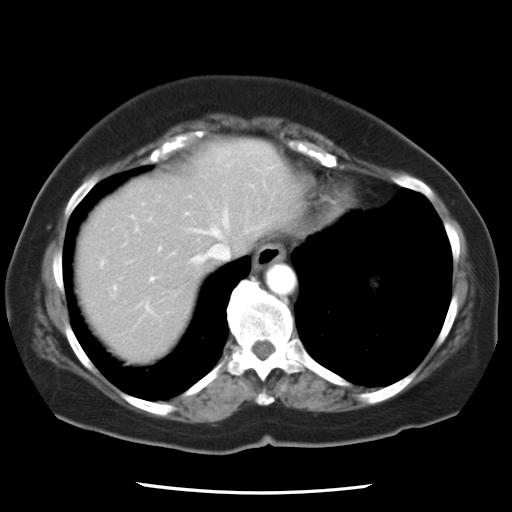
Contrast-enhanced abdominal CT, one axial slice. Position 21 of 24 along the scan axis. Reconstruction kernel STANDARD. Intravenous contrast given. Soft-tissue window (W 400 / L 40 HU). 7.5 mm slice thickness. 512 × 512 image matrix, field of view 312 × 312 mm. Female patient, age 71 years. From the clinical record (not read from this slice): diagnosis: colorectal cancer liver metastases, imaged before liver resection; multiple liver metastases: no; largest metastasis: 4.3 cm; disease in both lobes: no.
Annotated regions visible in this slice (expert manual segmentation):
- hepatic veins: bounding box (x1, y1, x2, y2) in pixels: (186, 213, 264, 265)
- liver: (75, 139, 302, 358)
- planned liver remnant (the part of the liver to remain after resection): (75, 166, 248, 359)
- portal vein (with intrahepatic branches): (132, 148, 254, 281)